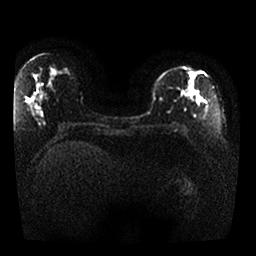
Breast MRI, one axial slice. Slice 13 of 25 in the series (ordered by position). Diffusion-weighted series; image 2 of 4 stored at this slice position (different b-values; order by instance number). 1.5 T. 4 mm slice thickness. 256 × 256 image matrix, field of view 330 × 330 mm. Female patient.
Structures marked on this image (manually delineated by an expert):
- tumour on diffusion-weighted imaging: bounding box <176,86,199,97> (left, top, right, bottom; pixels)